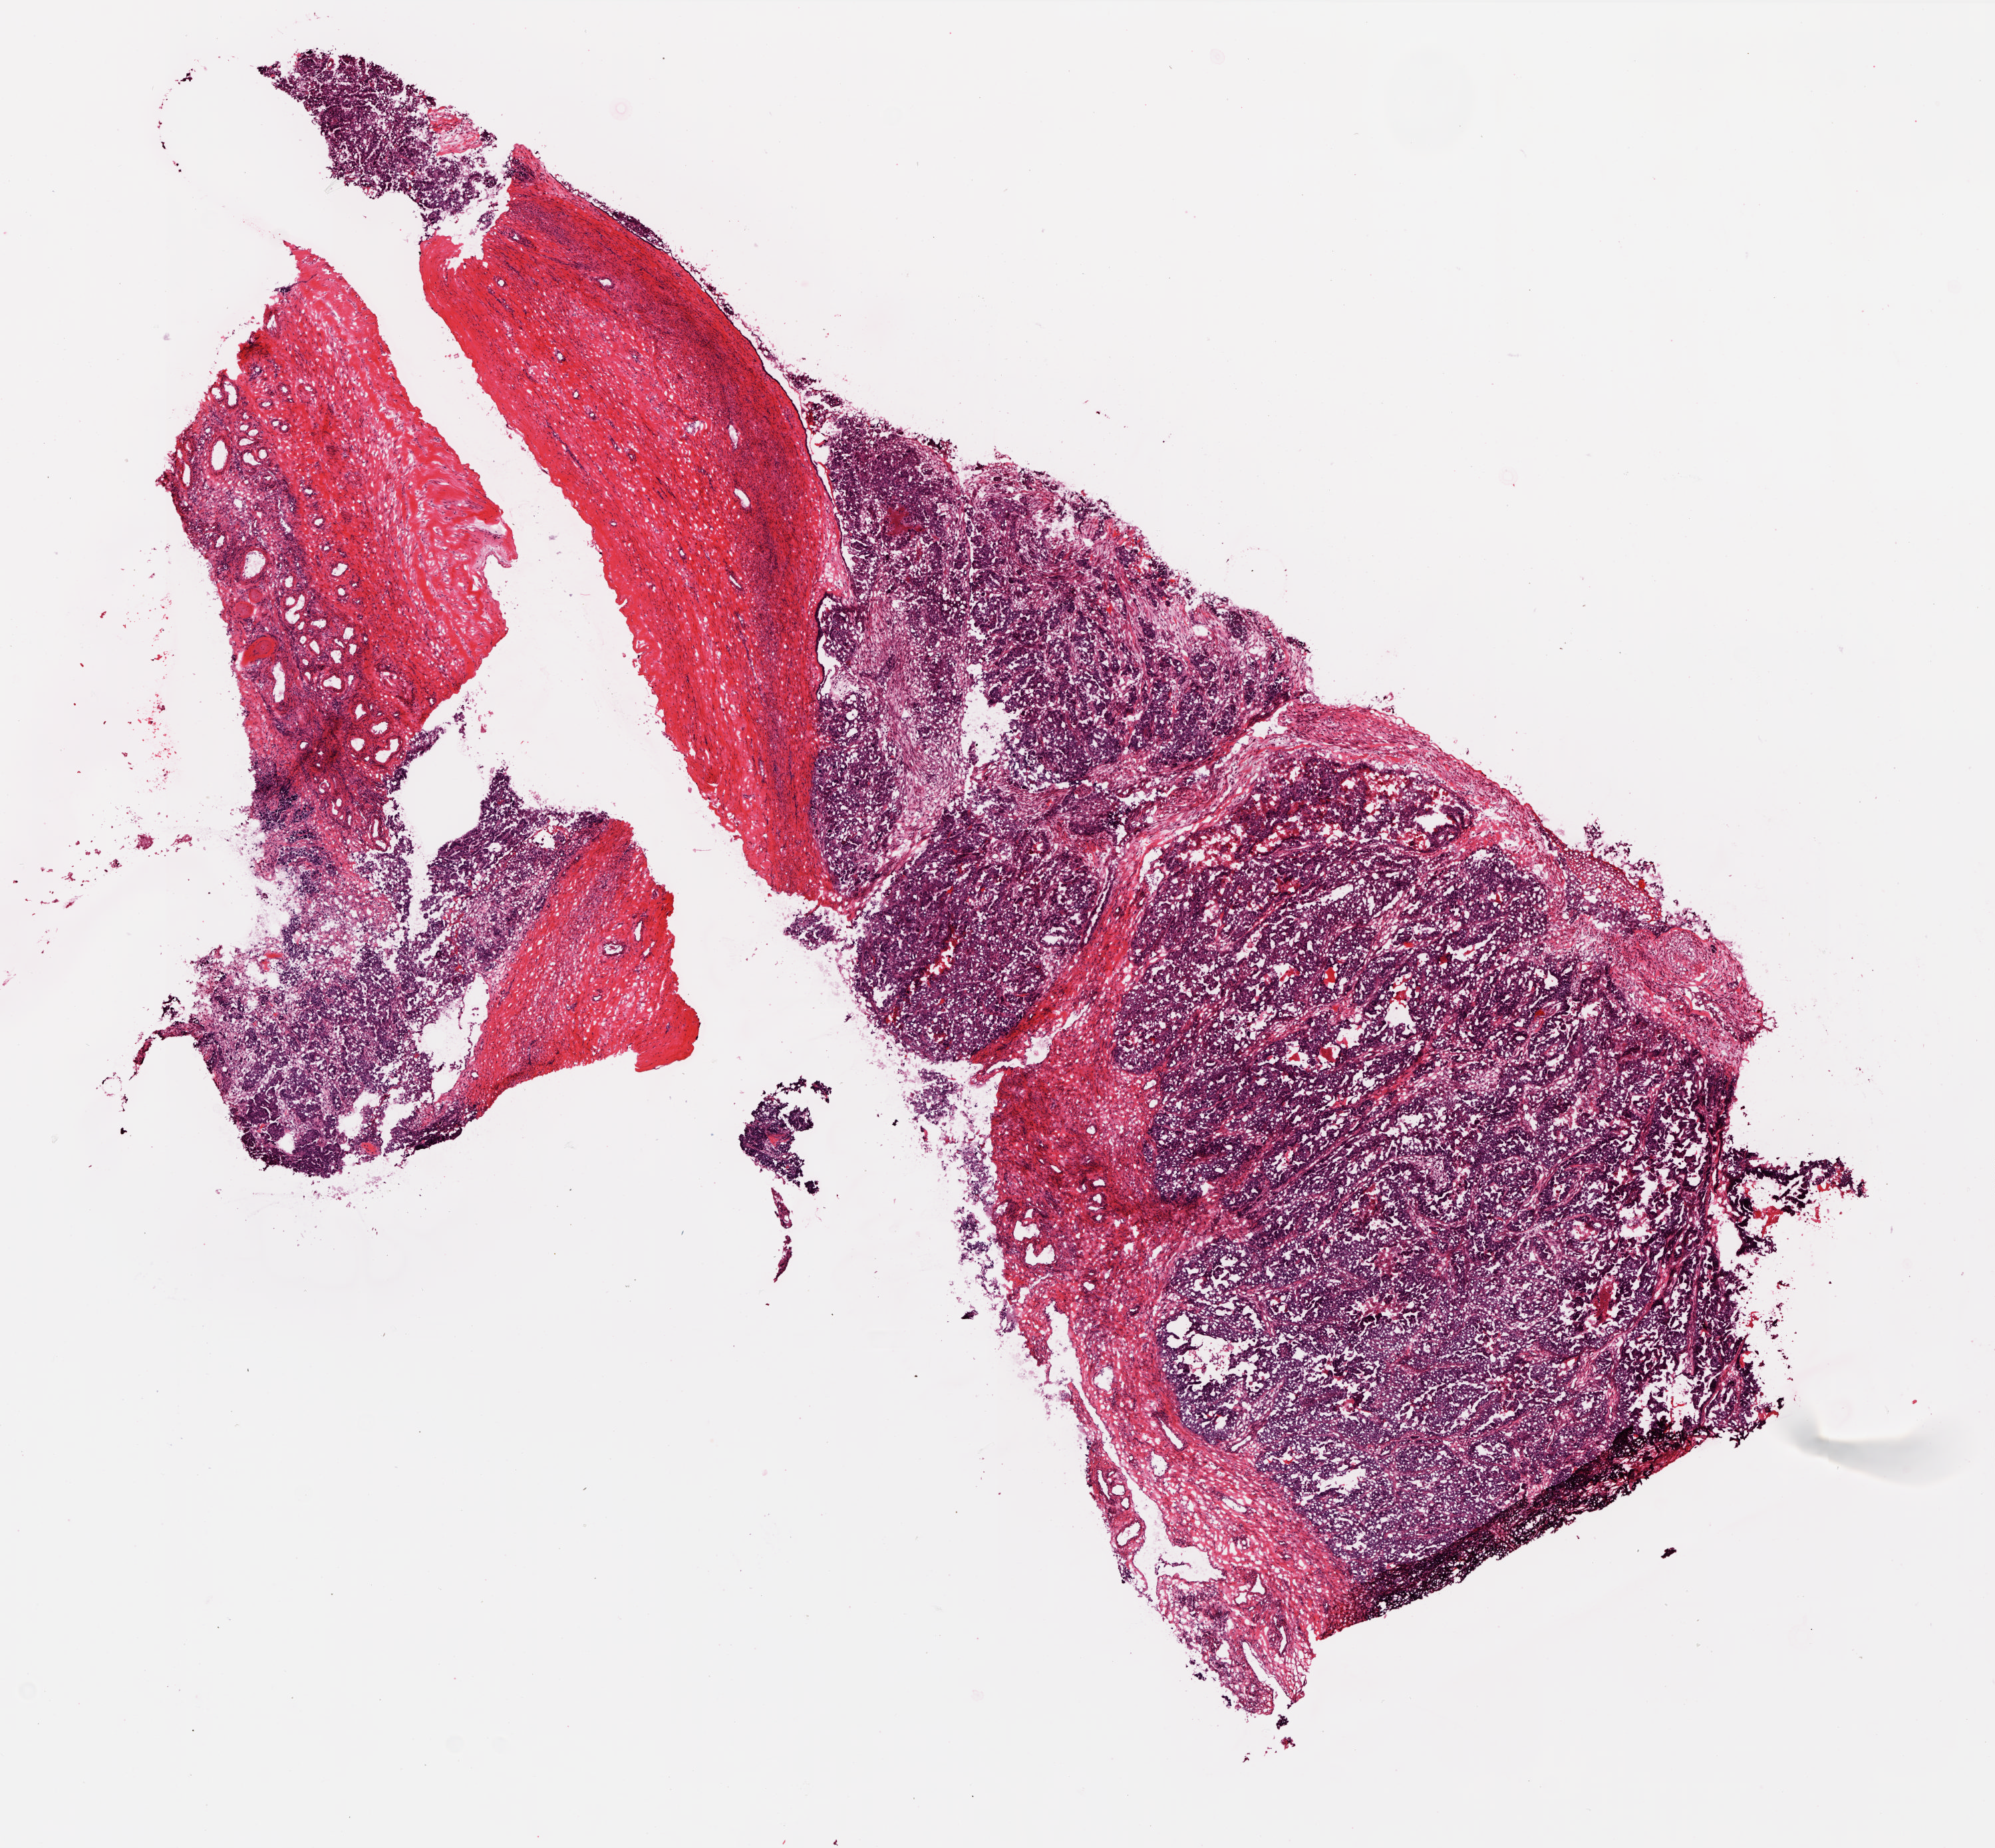
Whole-slide histology image, Hematoxylin and eosin (H&E) stained — shown as a low-resolution overview of the whole scanned area (about 12.0 x 11.1 mm, slide scanned at 20x); frozen section; primary tumour sample from the ovary. Female patient; age at initial diagnosis 70 years. Histologic grade: G3 (poorly differentiated). Slide review estimates, as recorded: tumour cells 8%, tumour nuclei 90%, normal cells 0%, stromal cells 89%, necrosis 3%.
Laterality: bilateral. FIGO stage: IIIC. Pathologic diagnosis: Serous cystadenocarcinoma, NOS.